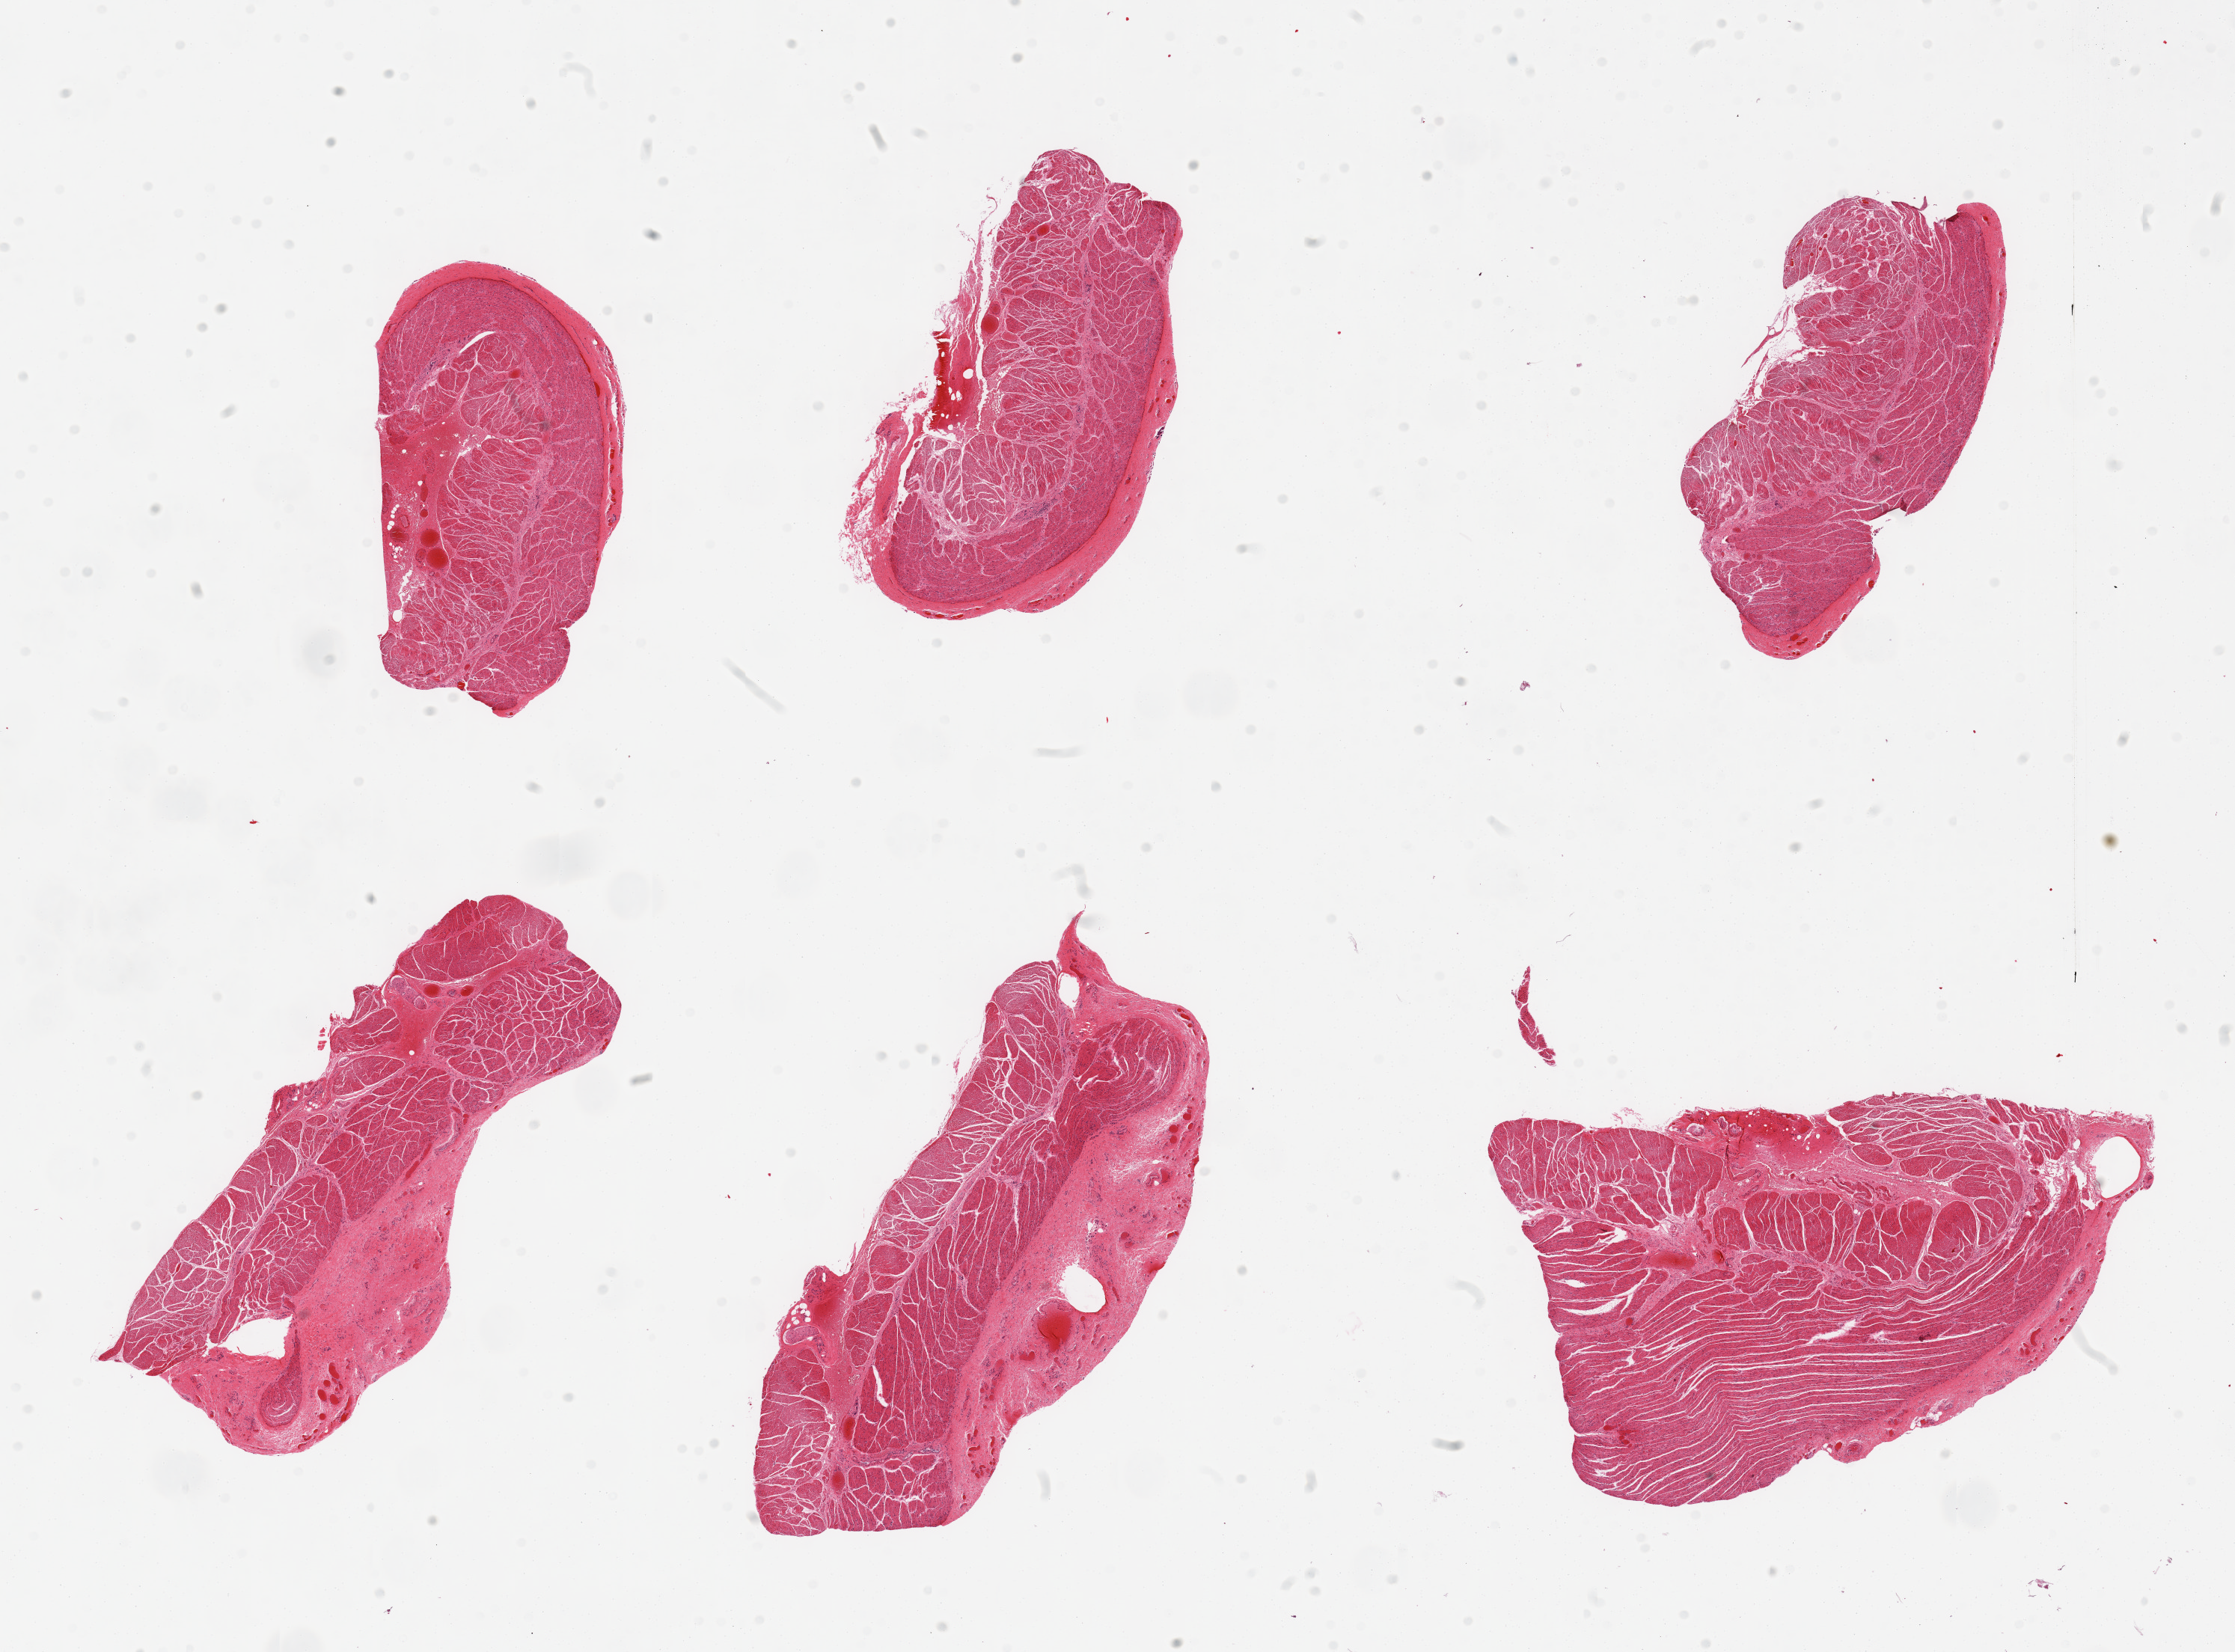
Hematoxylin and eosin (H&E) whole-slide image, shown as a low-resolution overview of the whole scanned area (about 23.6 x 17.5 mm); PAXgene-fixed paraffin-embedded (PFPE) section; target tissue: esophageal muscle; donor tissue sample. Donor sex: male.
* review note (as recorded): 6 pieces, well trimmed